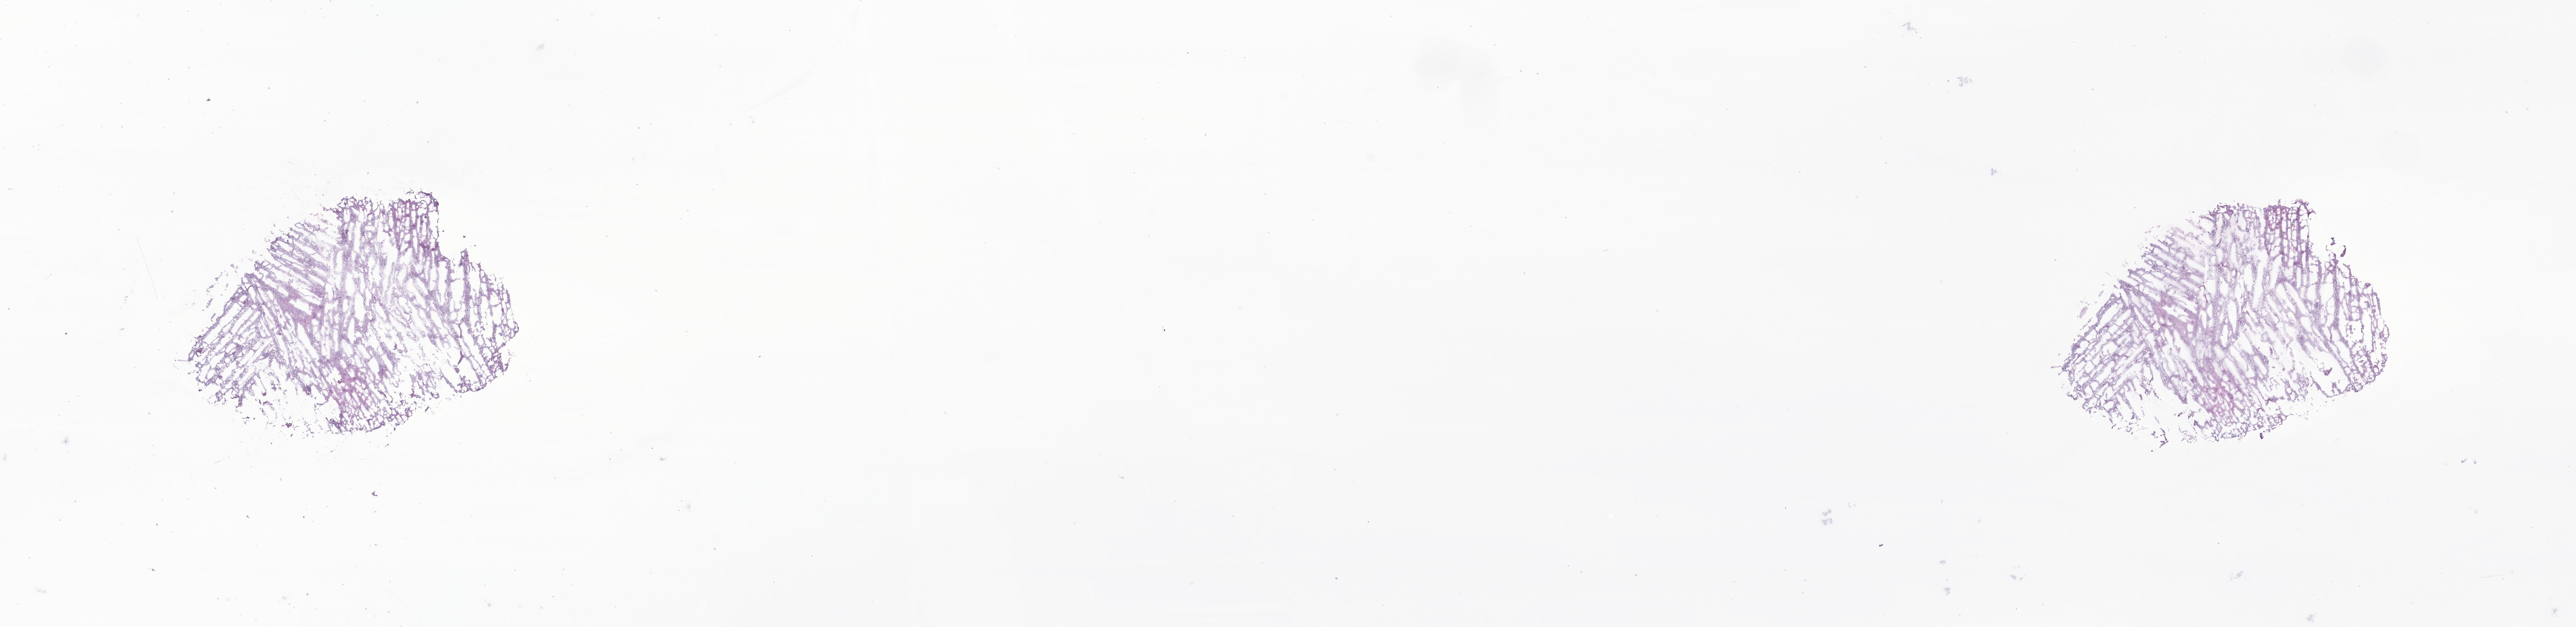
Whole-slide image, hematoxylin and eosin (H&E) stain of tumor tissue from the brain — whole scanned area (about 27.2 x 6.6 mm) shown as a low-resolution overview, frozen section (OCT-embedded). Patient: male, age 88 months (7 years 4 months).
* diagnosis (ICD-O-3 morphology term): Pilocytic astrocytoma